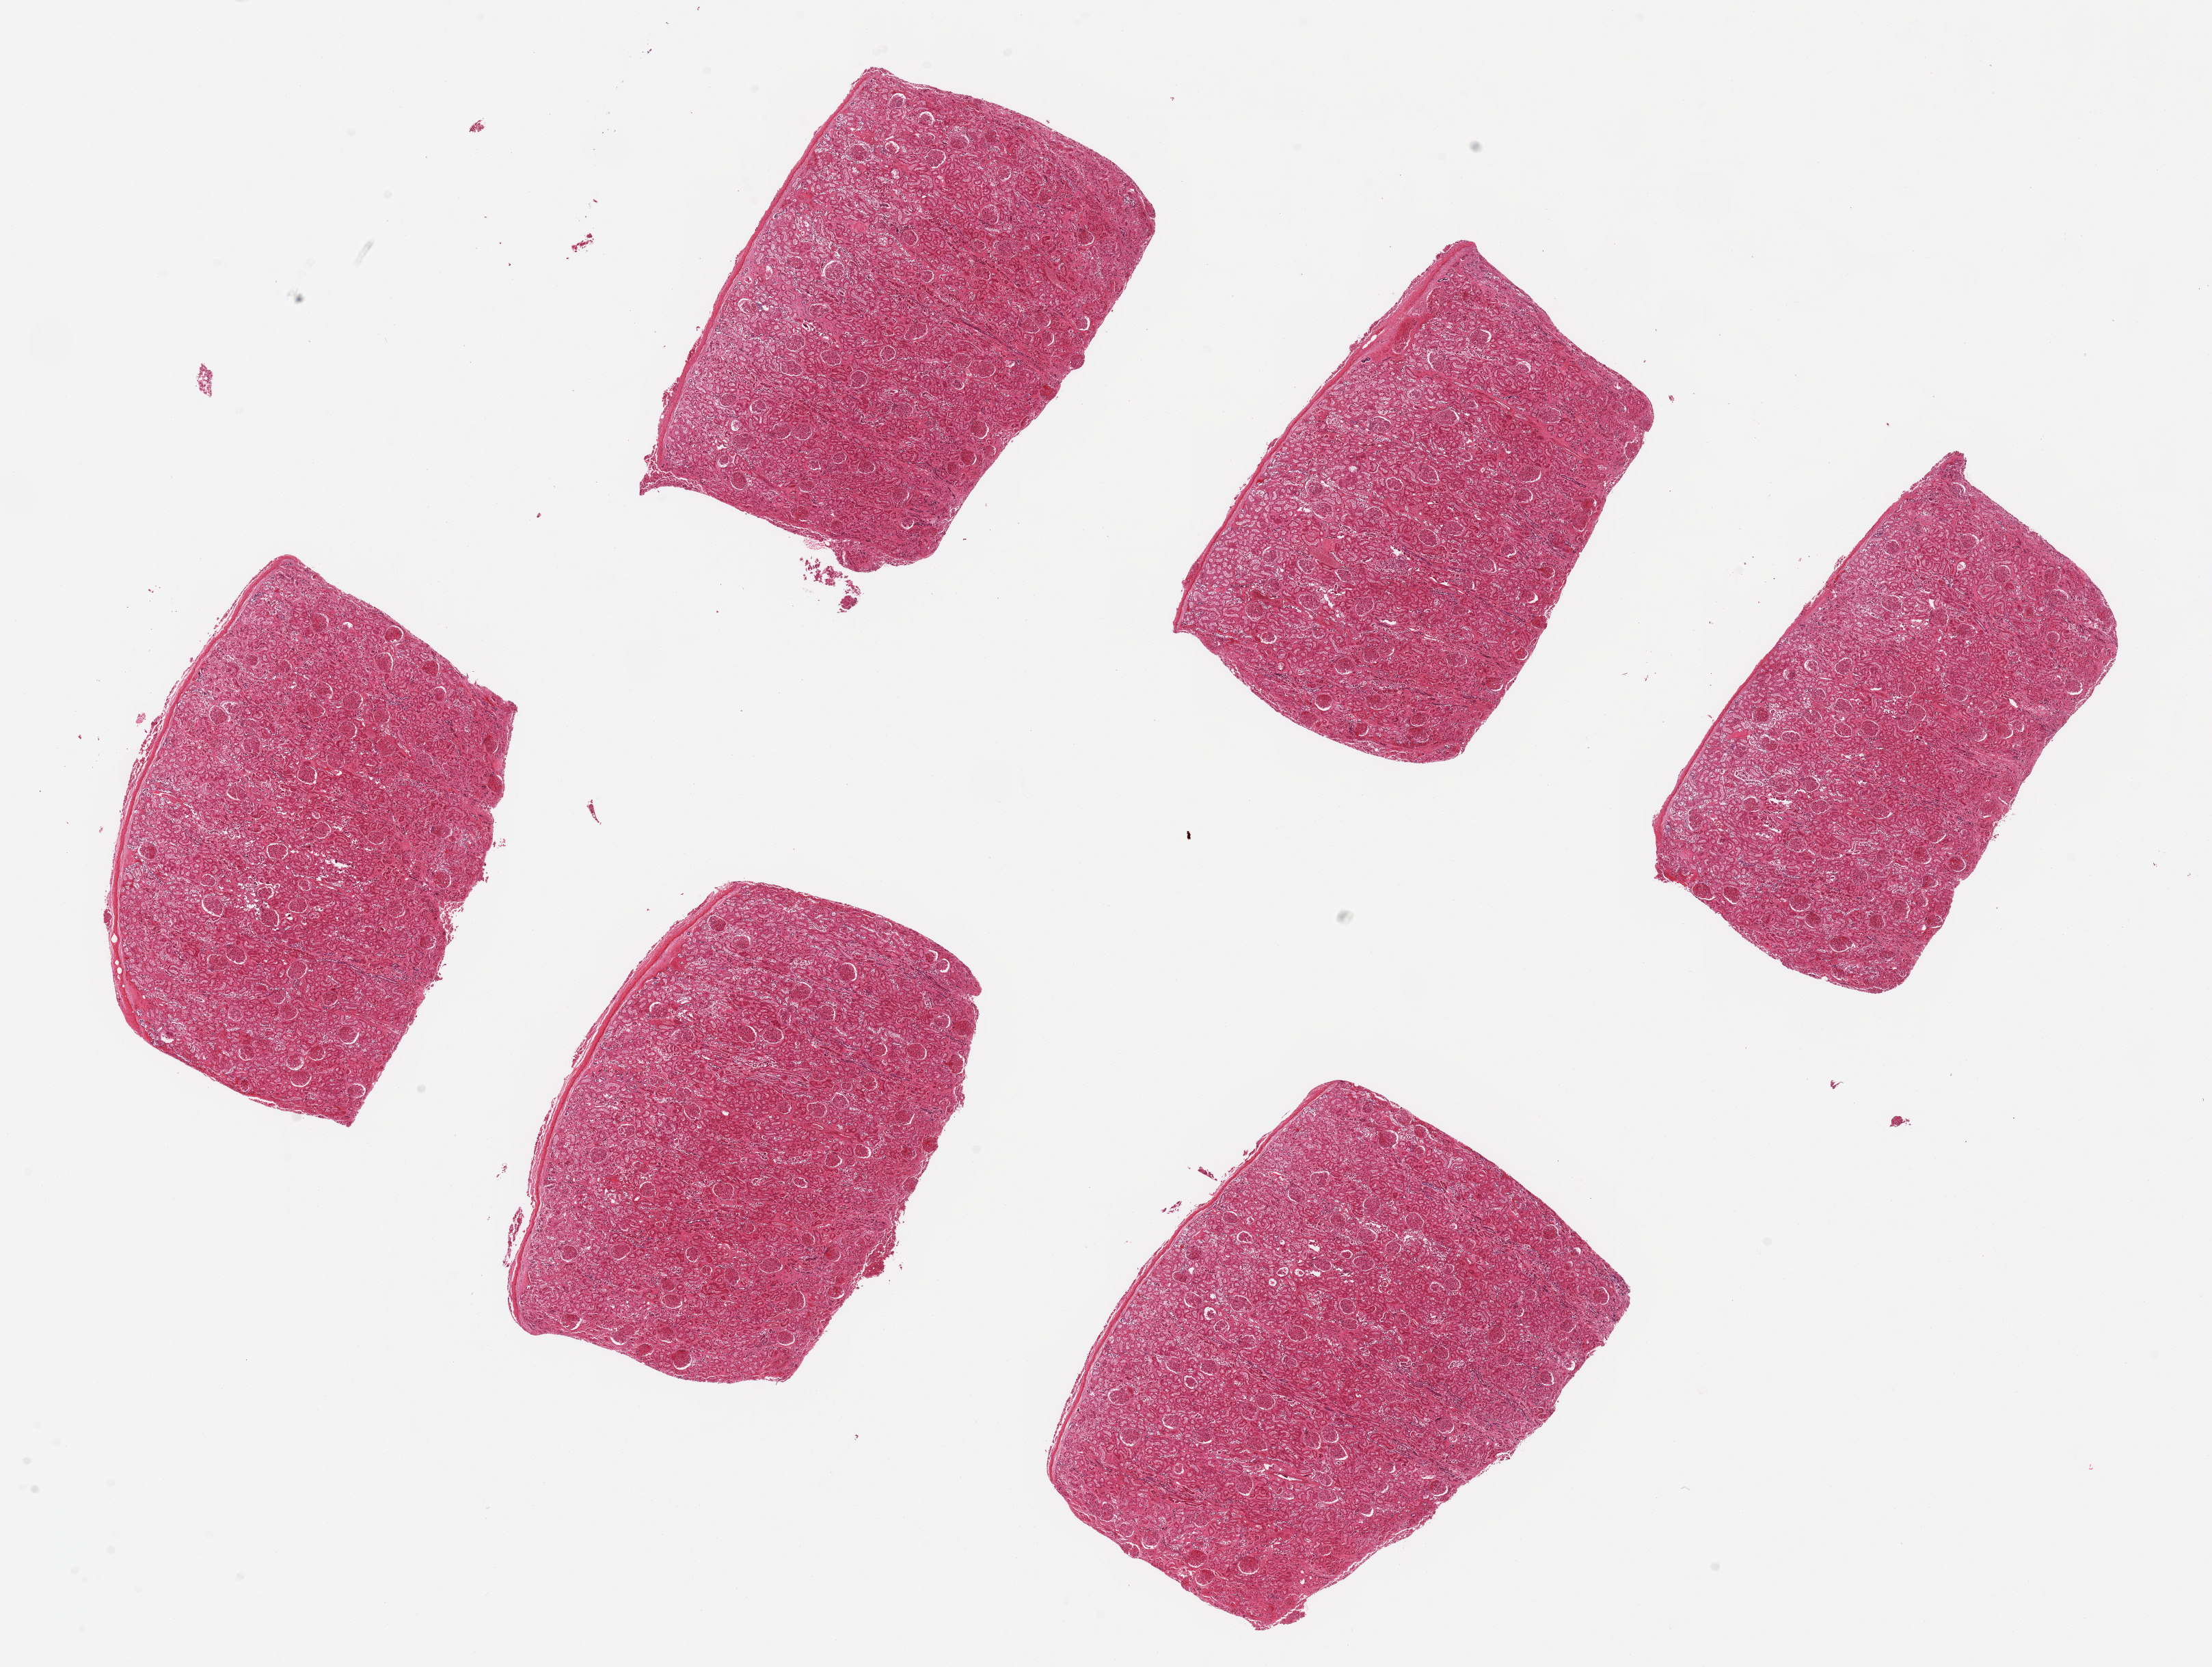
Whole-slide image, H&E stain, brightfield — low-resolution overview of the scanned area, about 25.6 x 19.3 mm; PAXgene-fixed, paraffin-embedded tissue; target tissue: renal cortex; donor tissue sample.
Reviewer comment on this tissue sample: 6 pieces,~5x5mm; no scarred glomeruli; moderately congested.